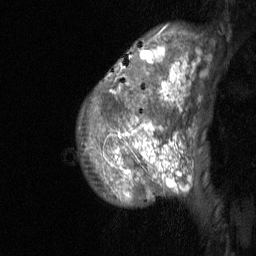
Breast MRI (dynamic contrast-enhanced), one sagittal slice; slice 47 of 64 in the series (ordered by position); dynamic contrast-enhanced study with each time point stored as its own series, time point 2 of 3 at this slice position (early post-contrast, ordered by acquisition time); 1.5 T; TE 4.8 ms, TR 27 ms; 256 × 256 image matrix, field of view 180 × 180 mm. Female patient, age 36 years. From the clinical record (not read from this slice): setting: breast cancer imaged before/during neoadjuvant chemotherapy; receptor status: HR-positive, HER2-negative.
Annotated regions visible in this slice (semi-automatically segmented with operator editing):
- analysis volume of interest (the breast-tissue region the enhancement analysis was run in; not a lesion): bounding box <77,25,210,207> (left, top, right, bottom; pixels)
- tumour enhancement mask (voxels above the 90 % enhancement threshold inside the analysis volume of interest): <112,47,192,192>